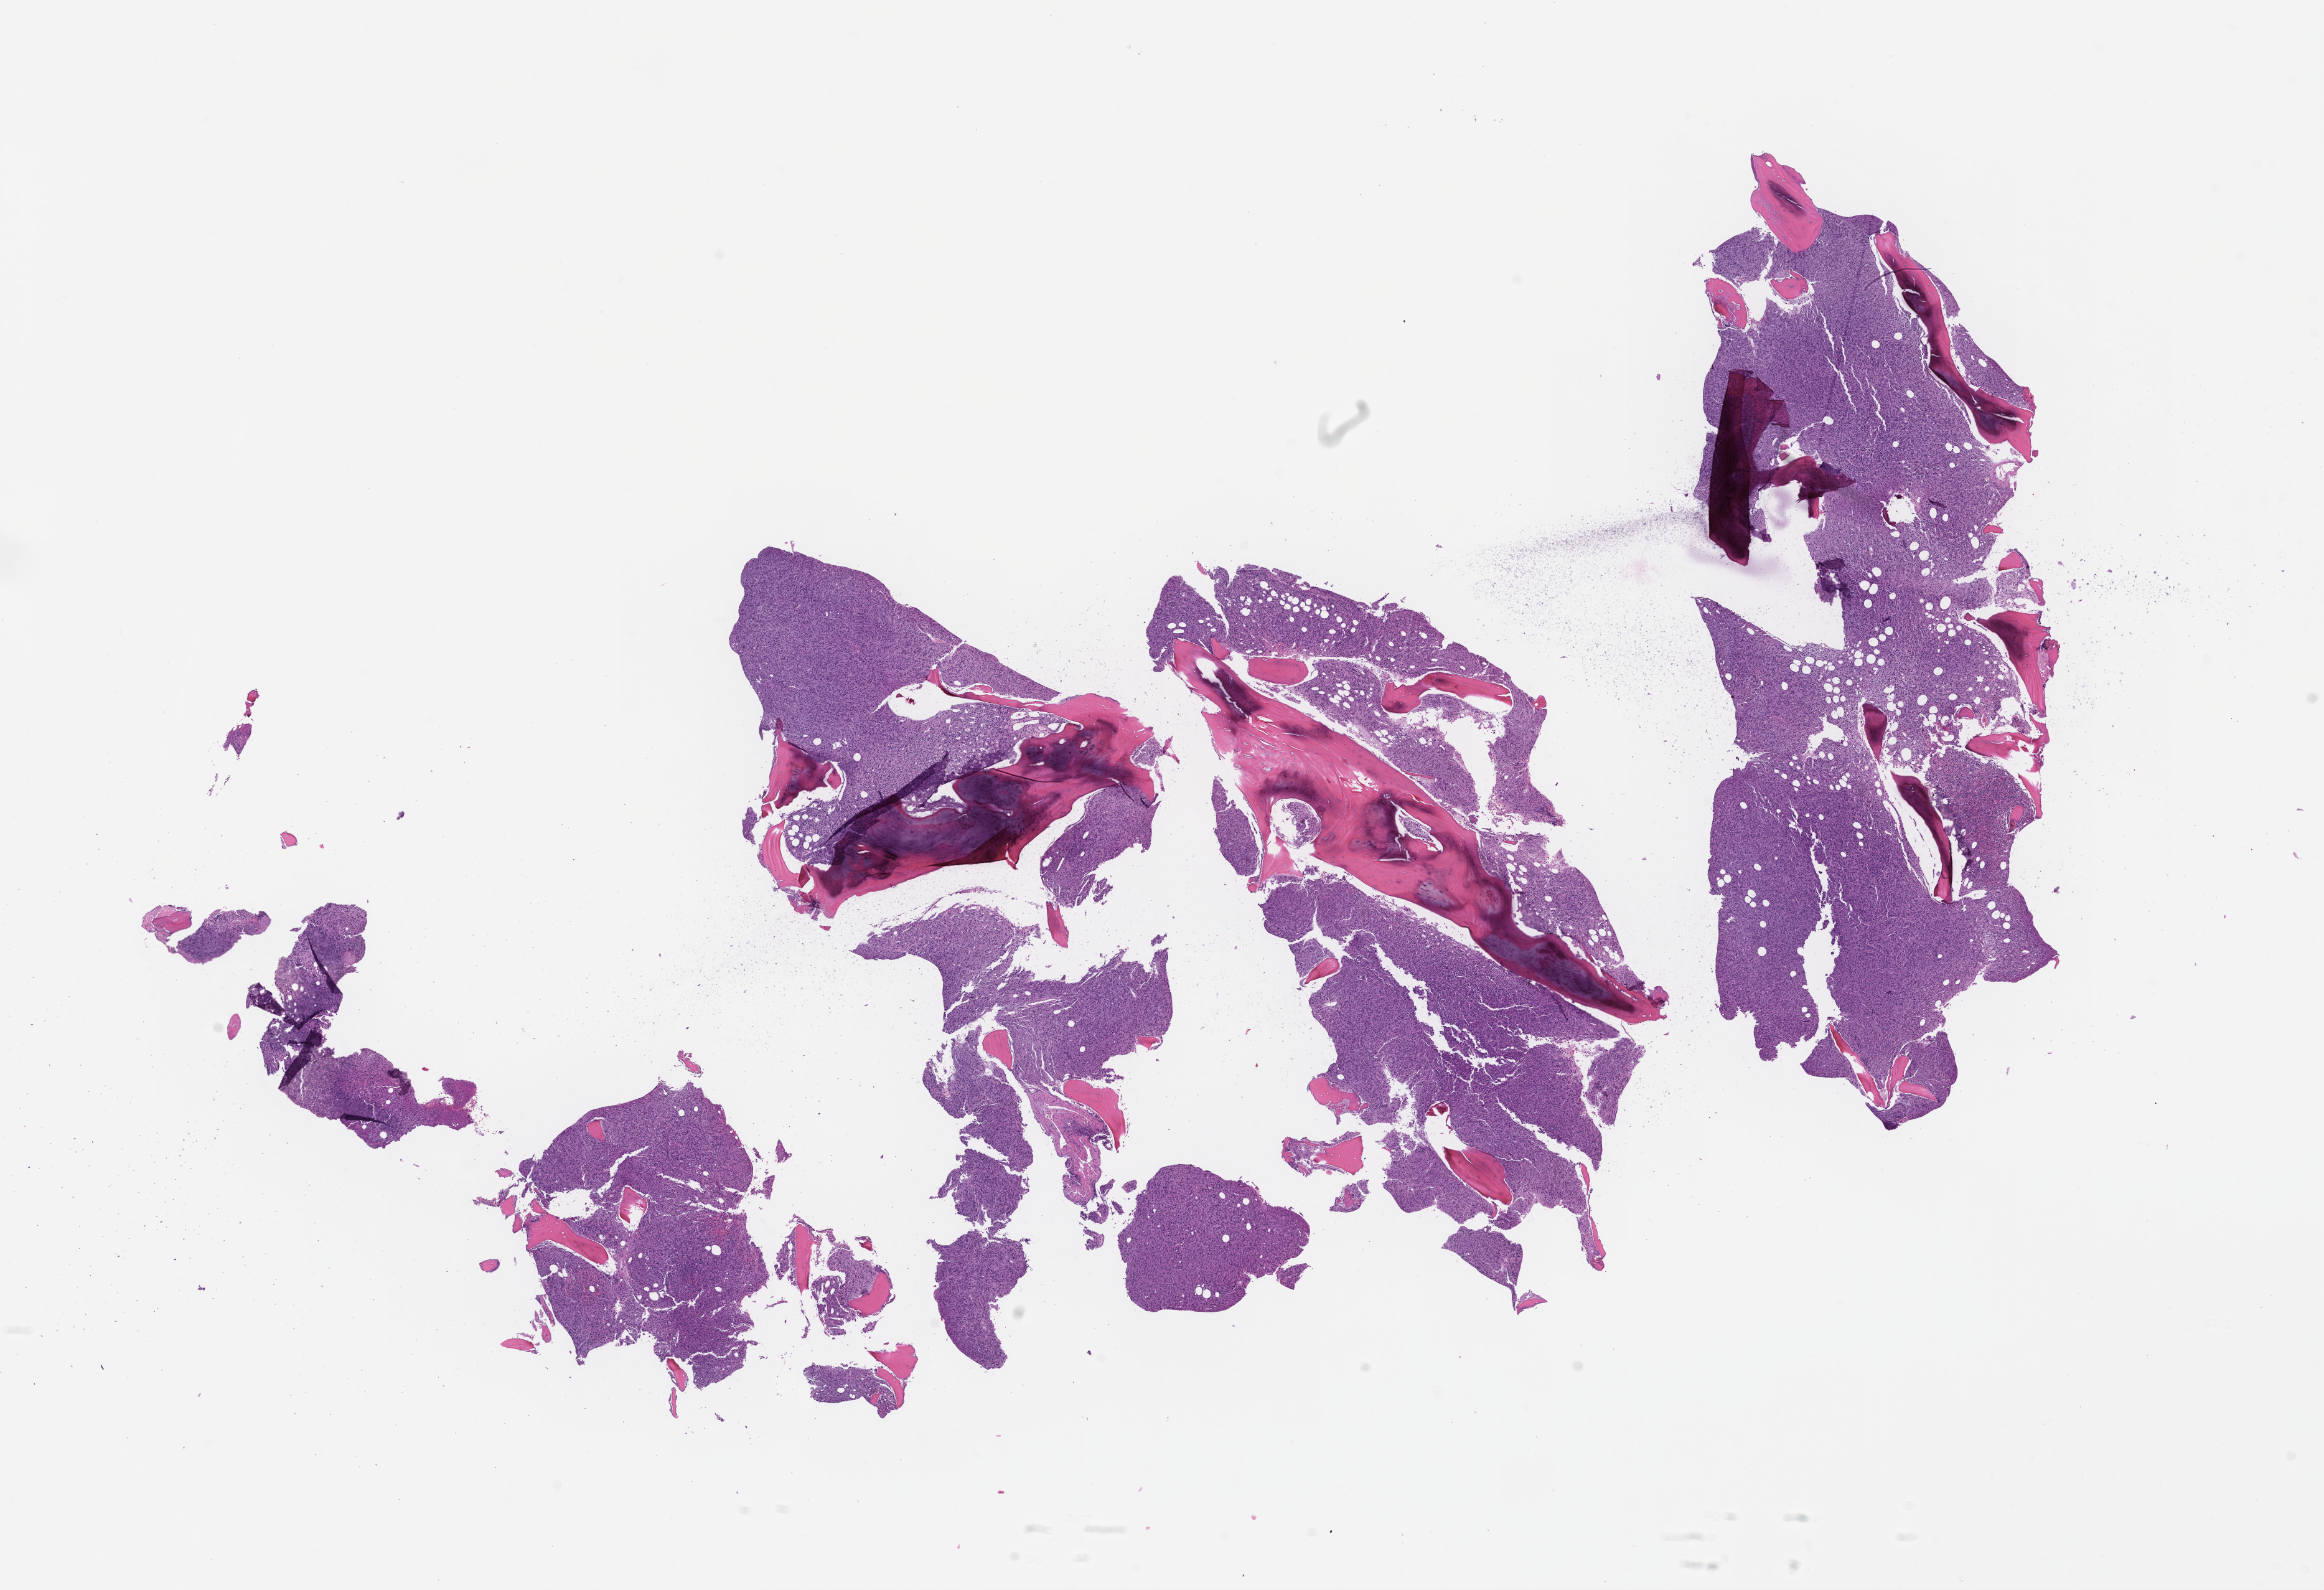
Digitized hematoxylin and eosin (H&E)-stained section — low-resolution overview of the scanned area, about 15.1 x 10.3 mm. Formalin-fixed, paraffin-embedded (FFPE) tissue. Patient sex: female.
- this section: metastasis (sampled organ not recorded)
- primary diagnosis of the patient: Plasma Cell Myeloma